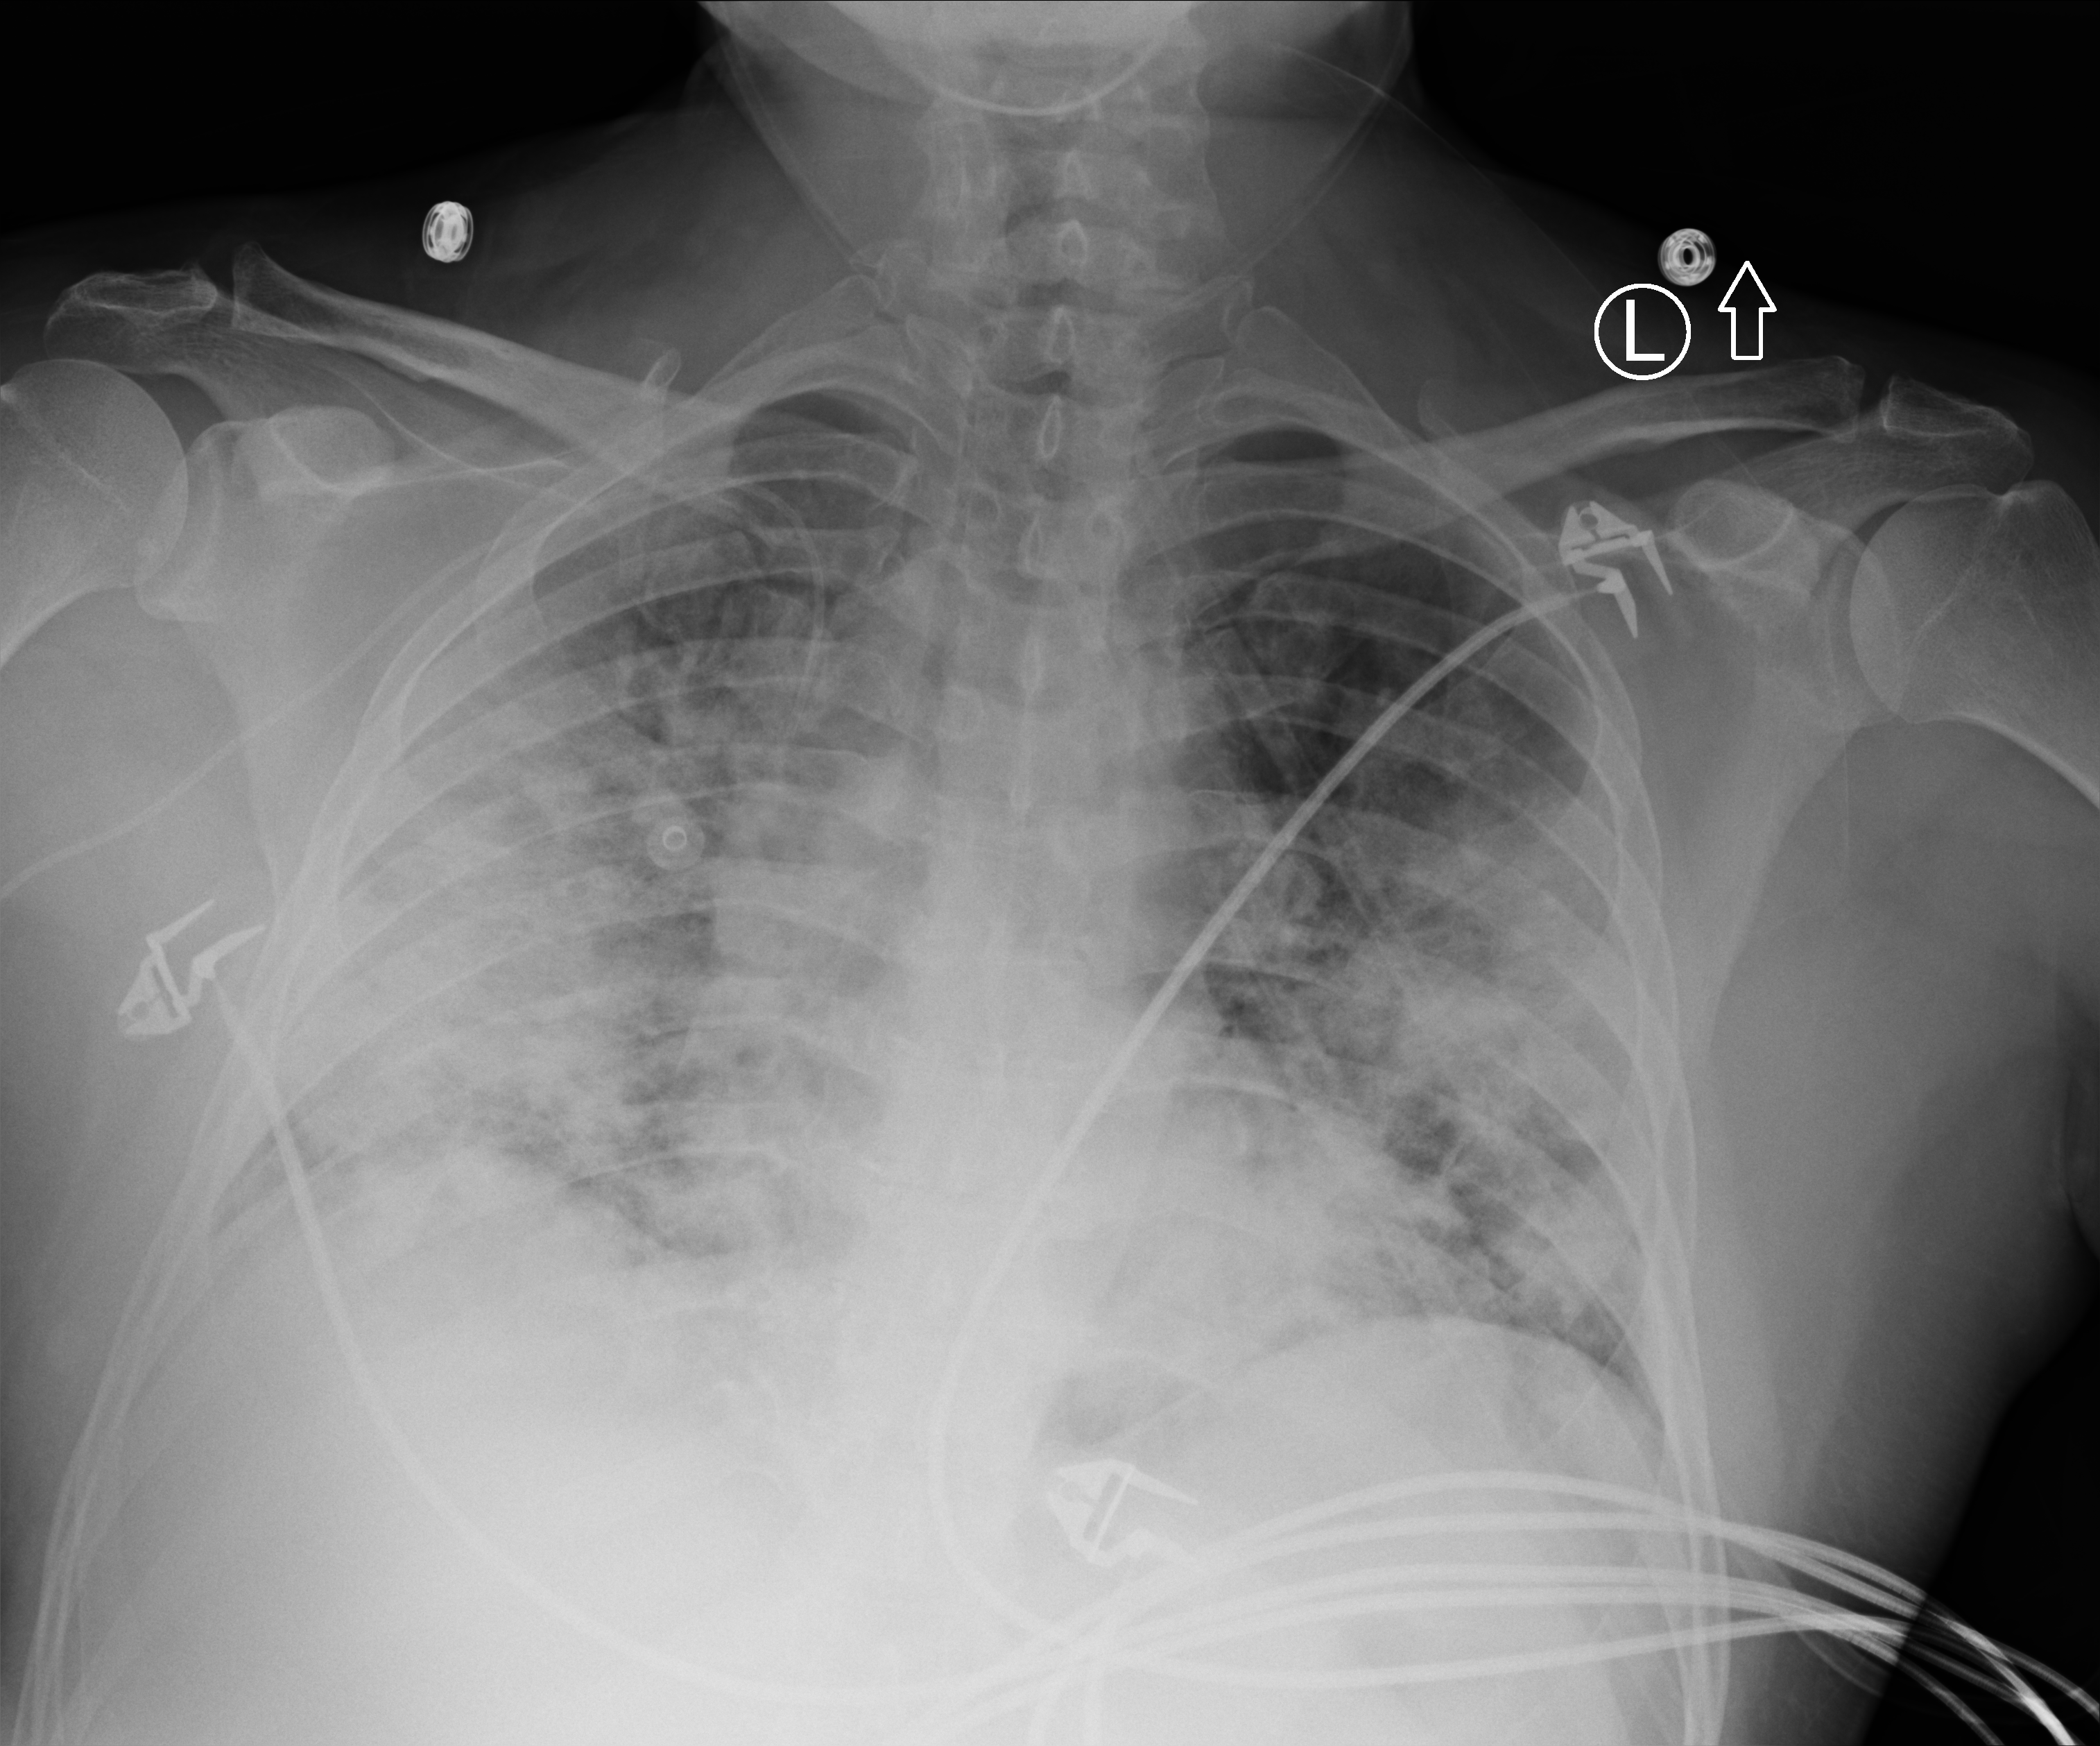
Bedside chest radiograph (computed radiography); anteroposterior (AP) projection. Male patient hospitalised with COVID-19, age 18–59 years.
From the hospital-stay record, not from the radiograph (when in the stay this image was taken is not recorded): other chronic lung disease (admission record): no.